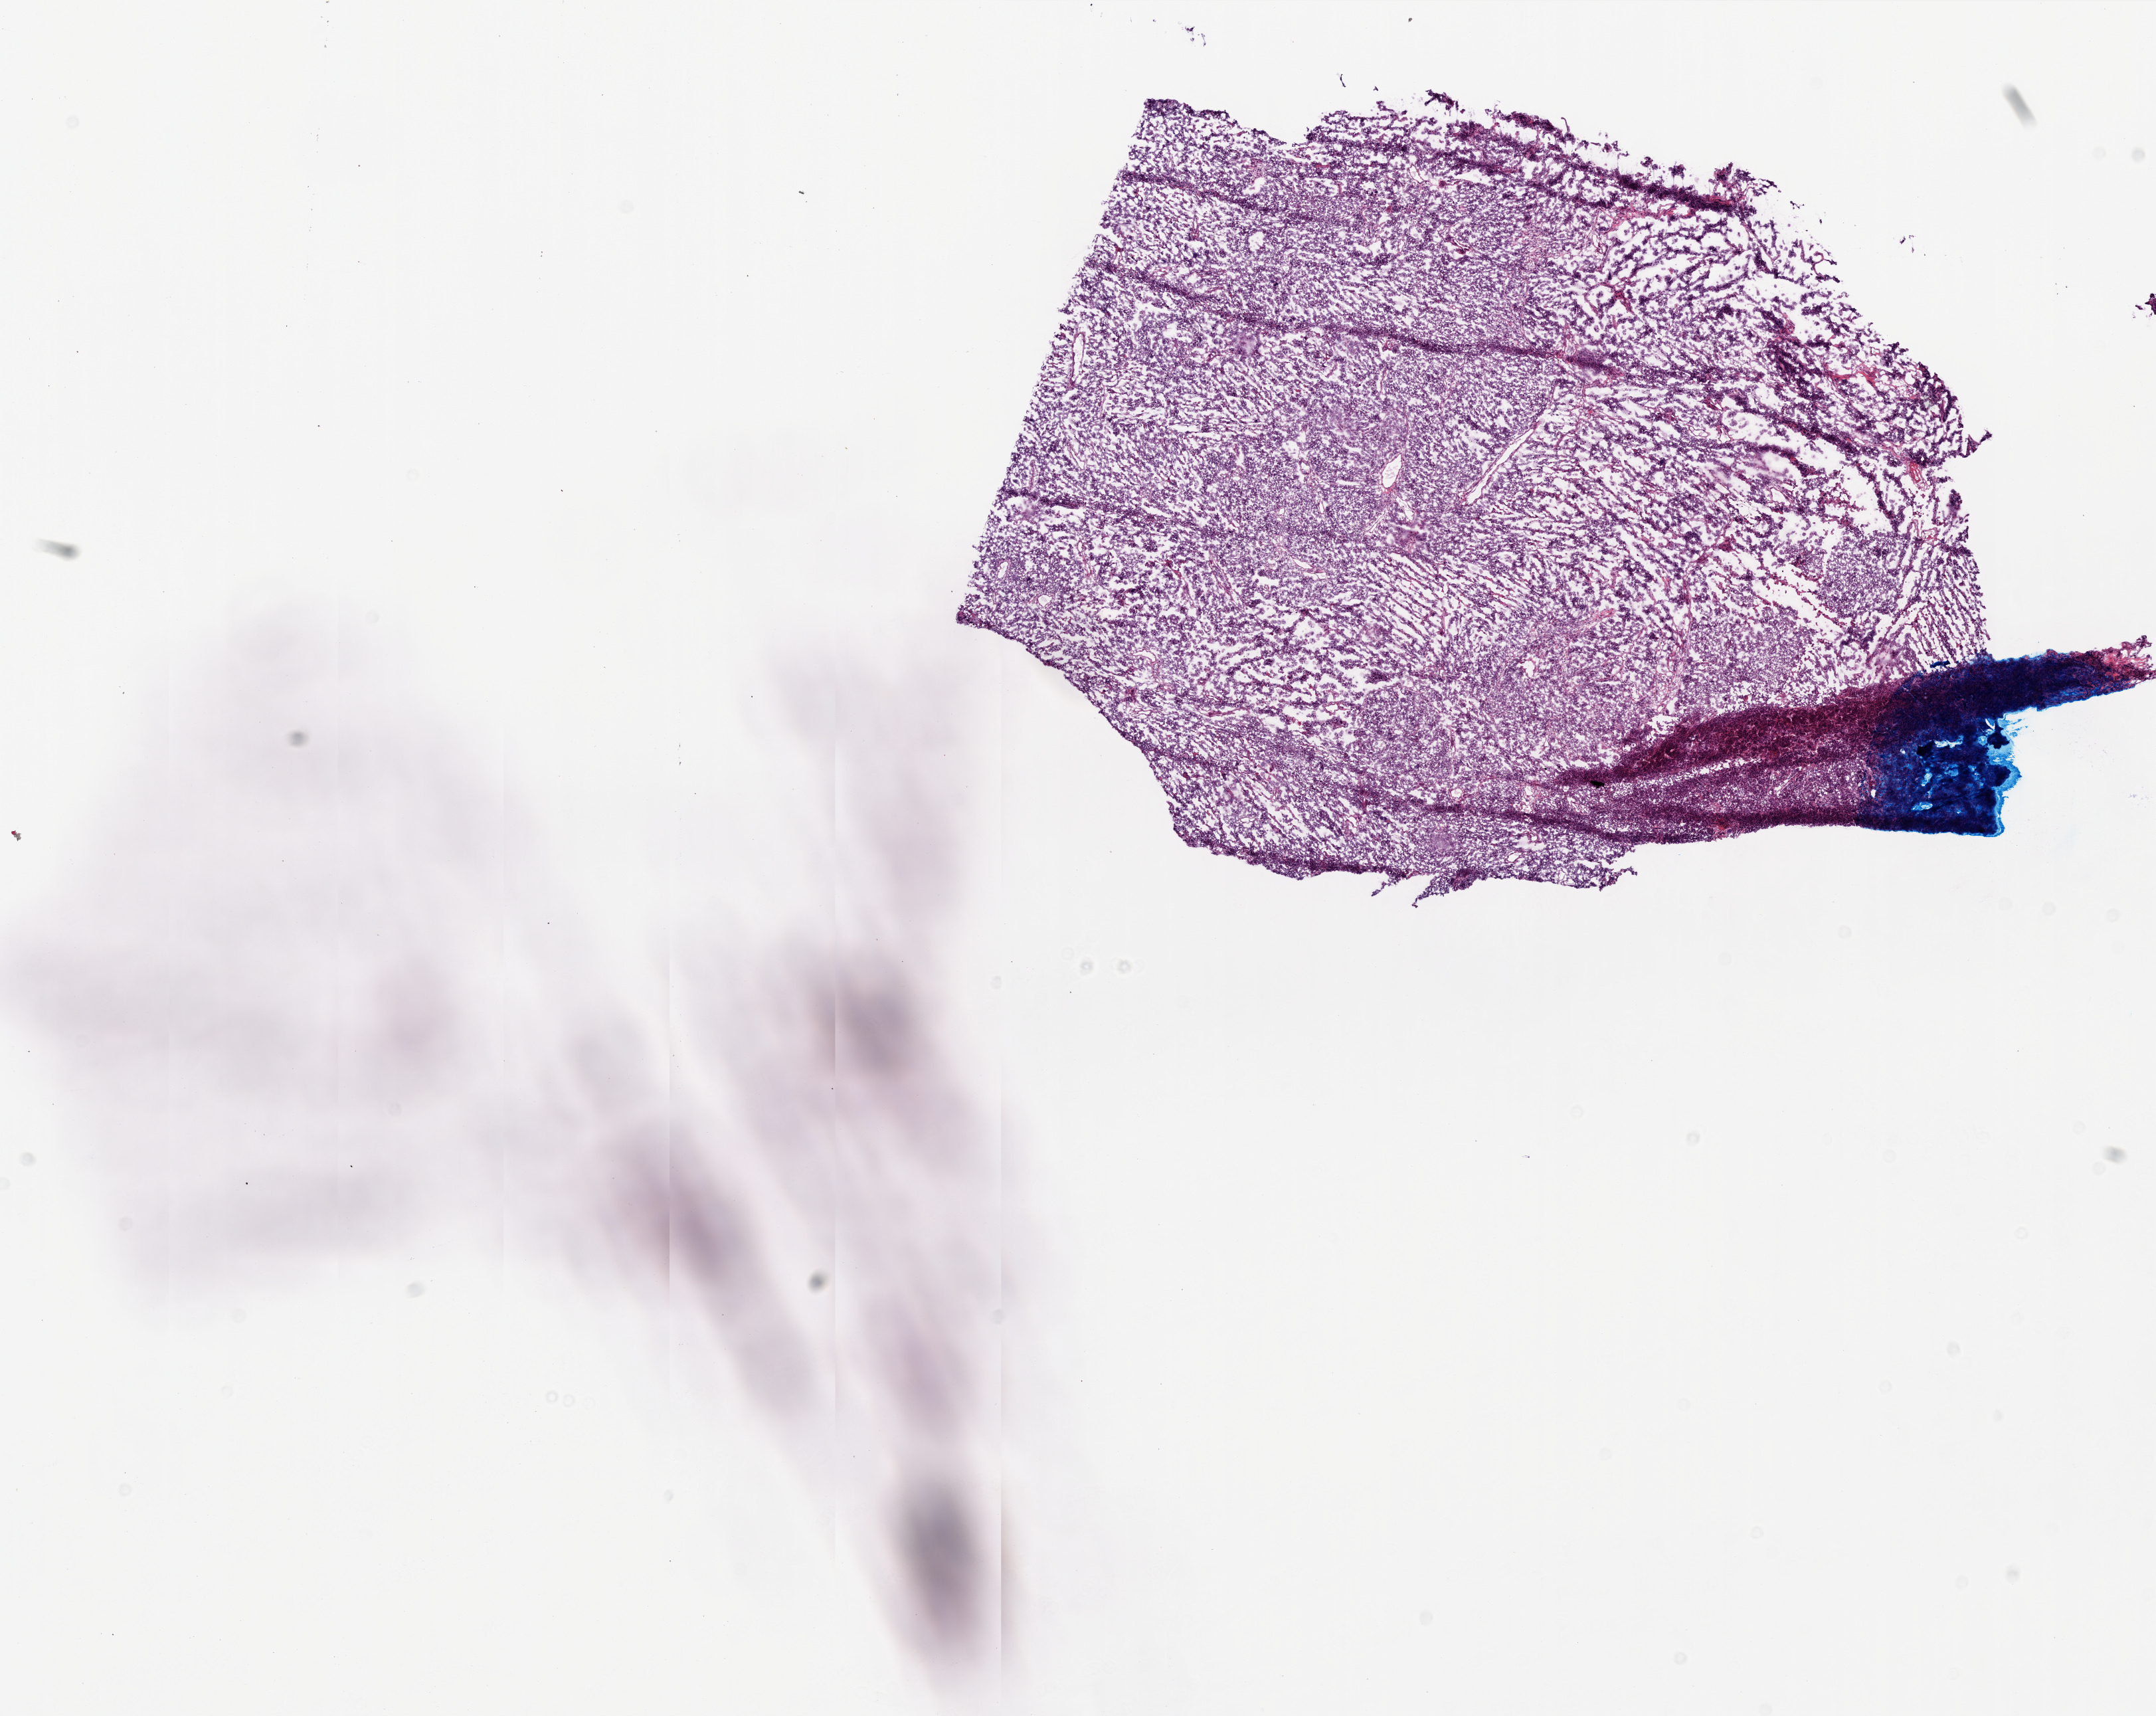
H&E-stained whole-slide image, shown as a low-resolution overview of the whole scanned area (about 13.0 x 10.3 mm); frozen section; ovary, primary tumour sample. Female patient; age at initial diagnosis 51 years. Histologic grade: G3 (poorly differentiated). Slide review estimates, as recorded: tumour cells 0%, tumour nuclei 95%, normal cells 0%, stromal cells 0%, necrosis 1%.
Laterality: left. FIGO stage: IIIC. Pathologic diagnosis: Serous cystadenocarcinoma, NOS.